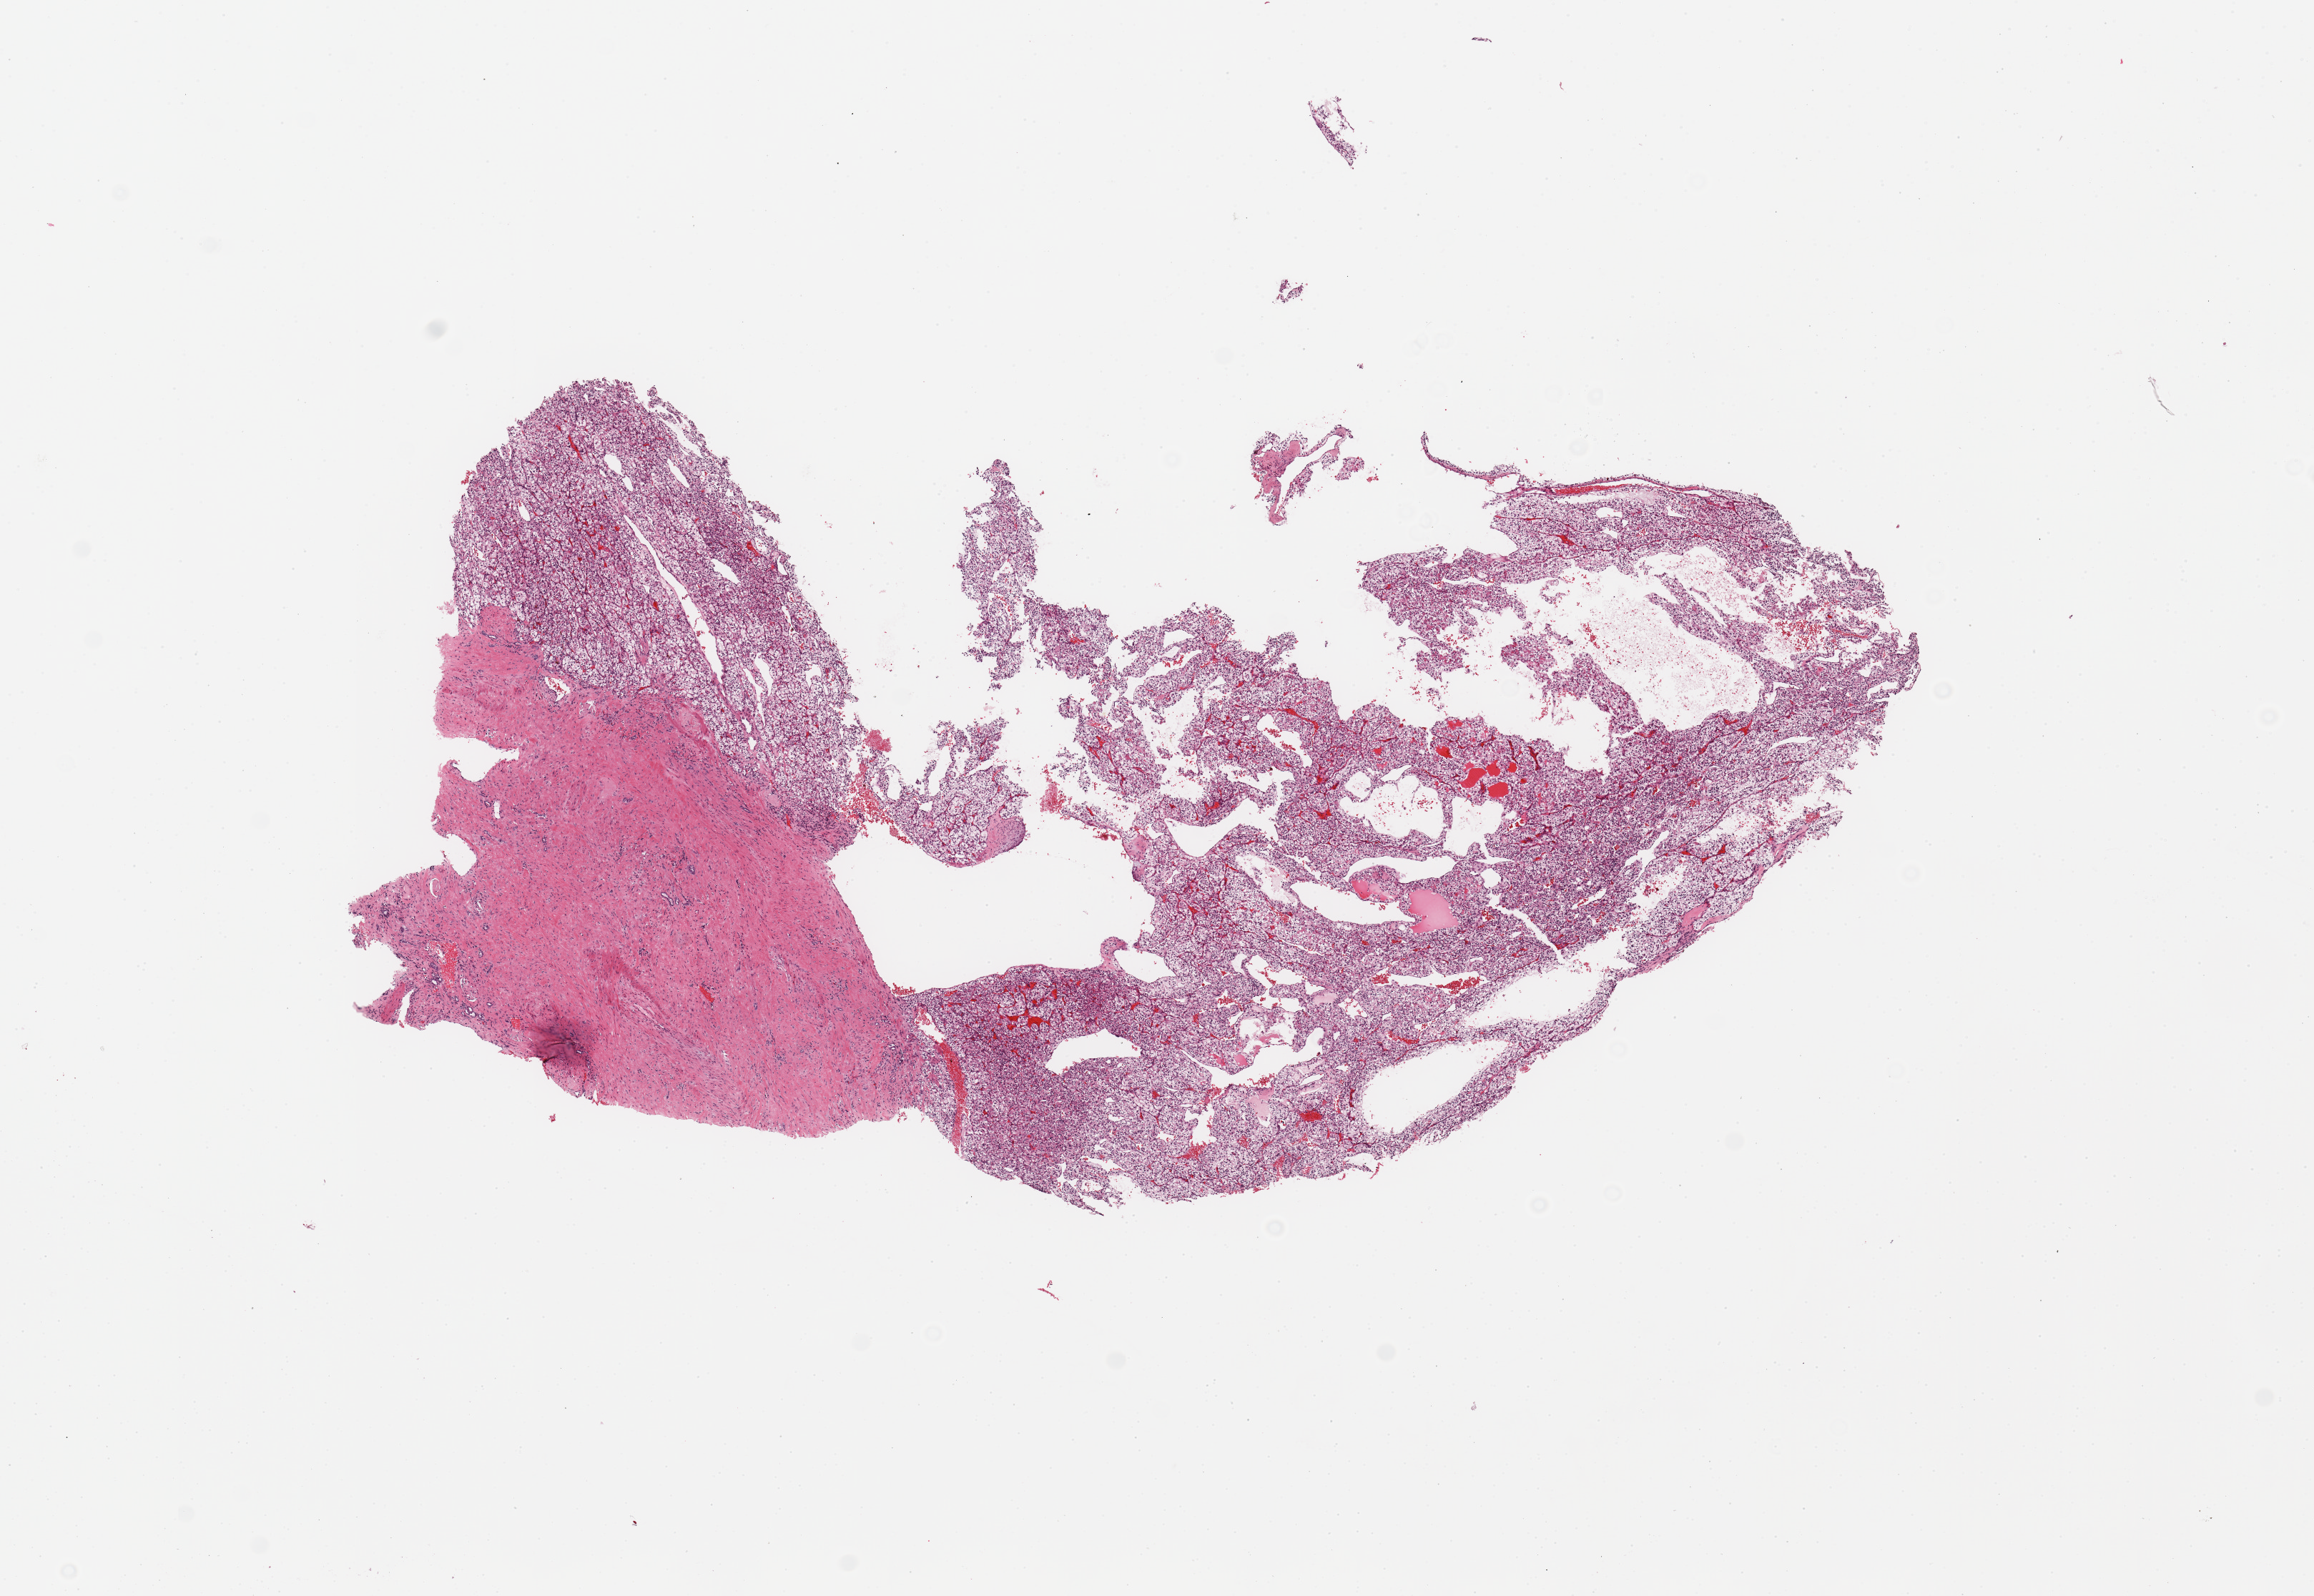
H&E whole-slide image — low-resolution overview of the scanned area, about 12.8 x 8.8 mm (from a 20x scan); tumour tissue sample, sampled site: kidney. Patient: female, age 75 years. Histologic grade: G3 (poorly differentiated). Composition of this section per pathologist review: tumour nuclei 90%, necrosis 0%.
Diagnosis: Renal cell carcinoma, NOS. AJCC pathologic stage: I. Primary tumour site (as recorded): upper pole.